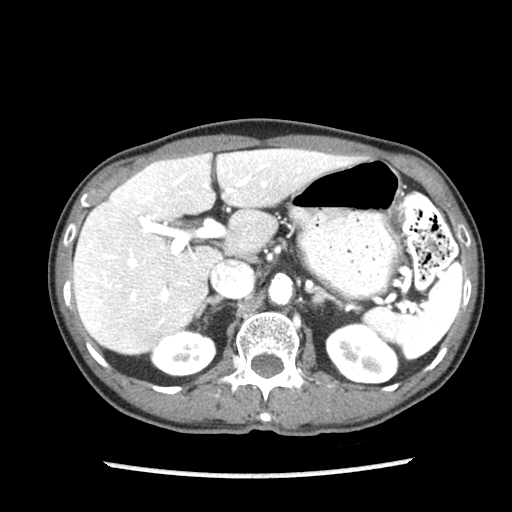
Contrast-enhanced abdominal CT (liver protocol), one axial slice; position 54 of 87 along the scan axis; 140 kVp; soft-tissue window (W 400 / L 40 HU); 512 × 512 image matrix, field of view 300 × 300 mm. From the clinical record (not read from this slice): diagnosis: hepatocellular carcinoma (patient treated with transarterial chemoembolisation; whether this scan precedes or follows treatment is not stated here); TNM stage (as recorded): Stage-IIIB; Child-Pugh class: A; tumour differentiation: well differentiated.
Structures marked on this image (semi-automatically segmented with operator editing):
- liver parenchyma outside the tumour (the mass and vessels are separate outlines, so this box may not span the whole liver): bounding box (x1, y1, x2, y2) in pixels: (72, 148, 357, 354)
- liver vessels: (89, 164, 301, 323)